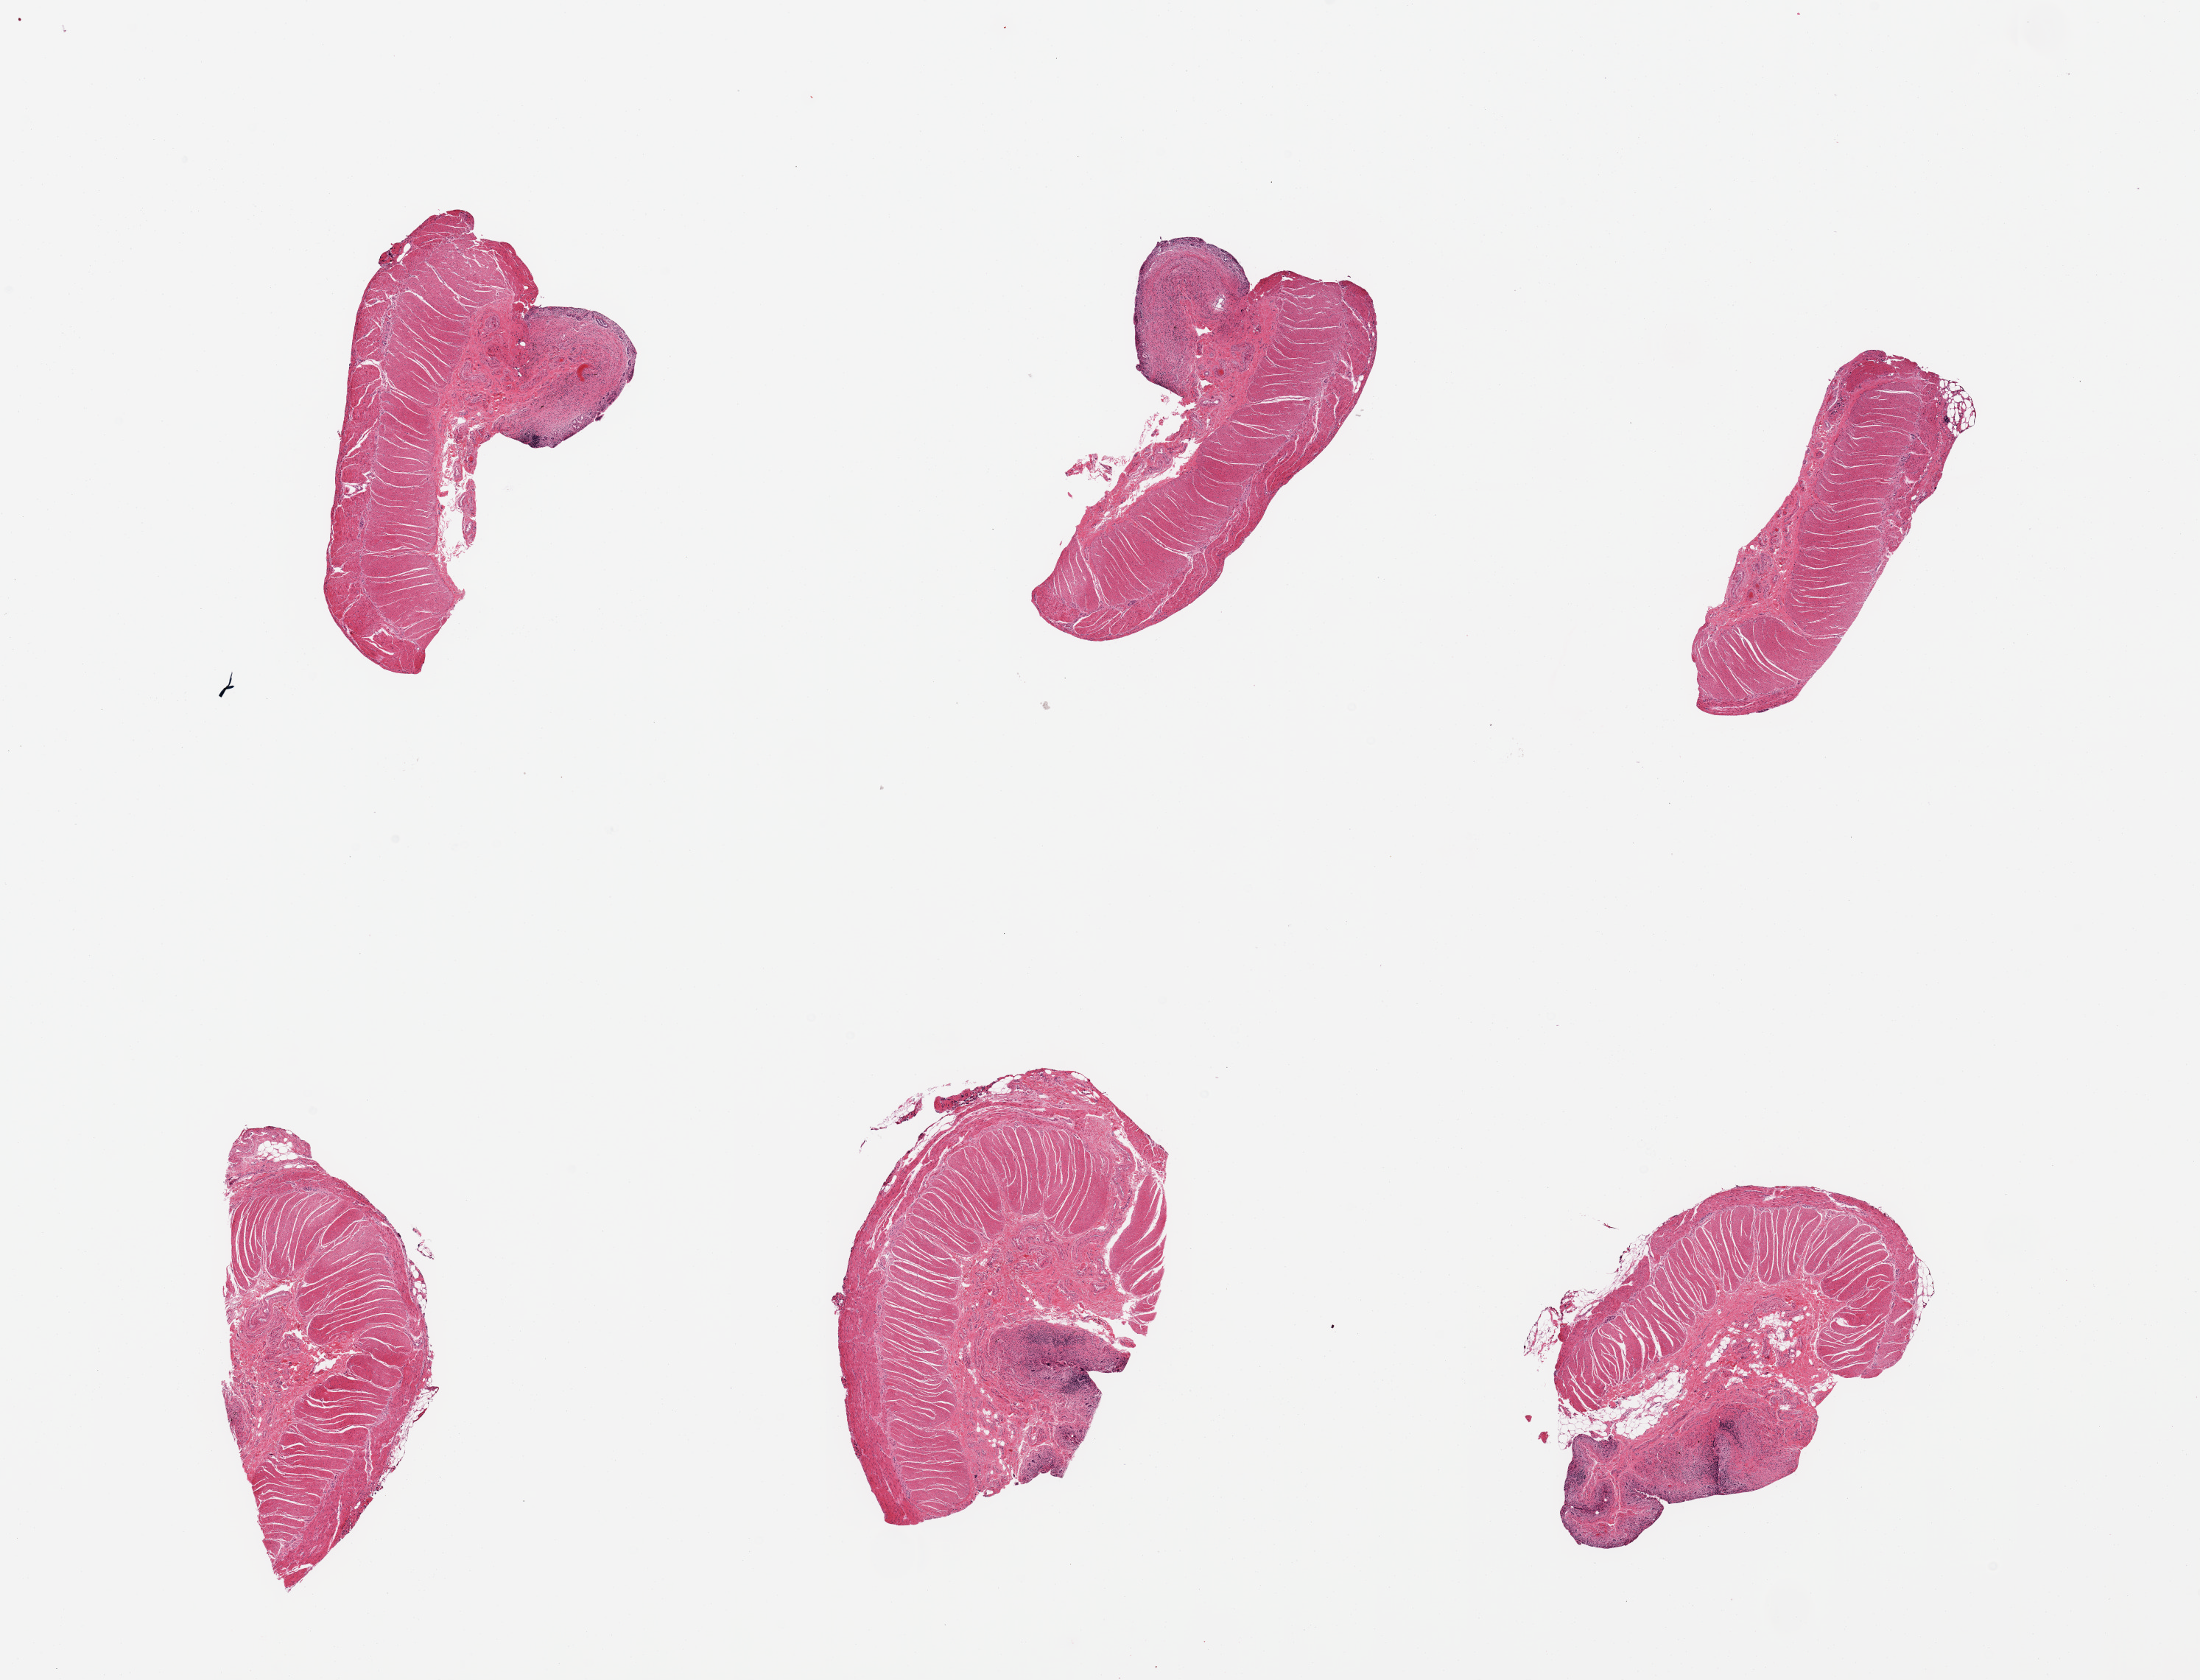
Digitized haematoxylin and eosin-stained section, brightfield — whole scanned area (about 23.6 x 18.0 mm, slide scanned at 20x) shown as a low-resolution overview, PAXgene-fixed, paraffin-embedded tissue, sampled site (target tissue): ileum, tissue donor sample.
Review note (as recorded): 6 pieces; autolyzed mucosa with minimal lymphoid tissue; specimens have full thickness of ileal wall.